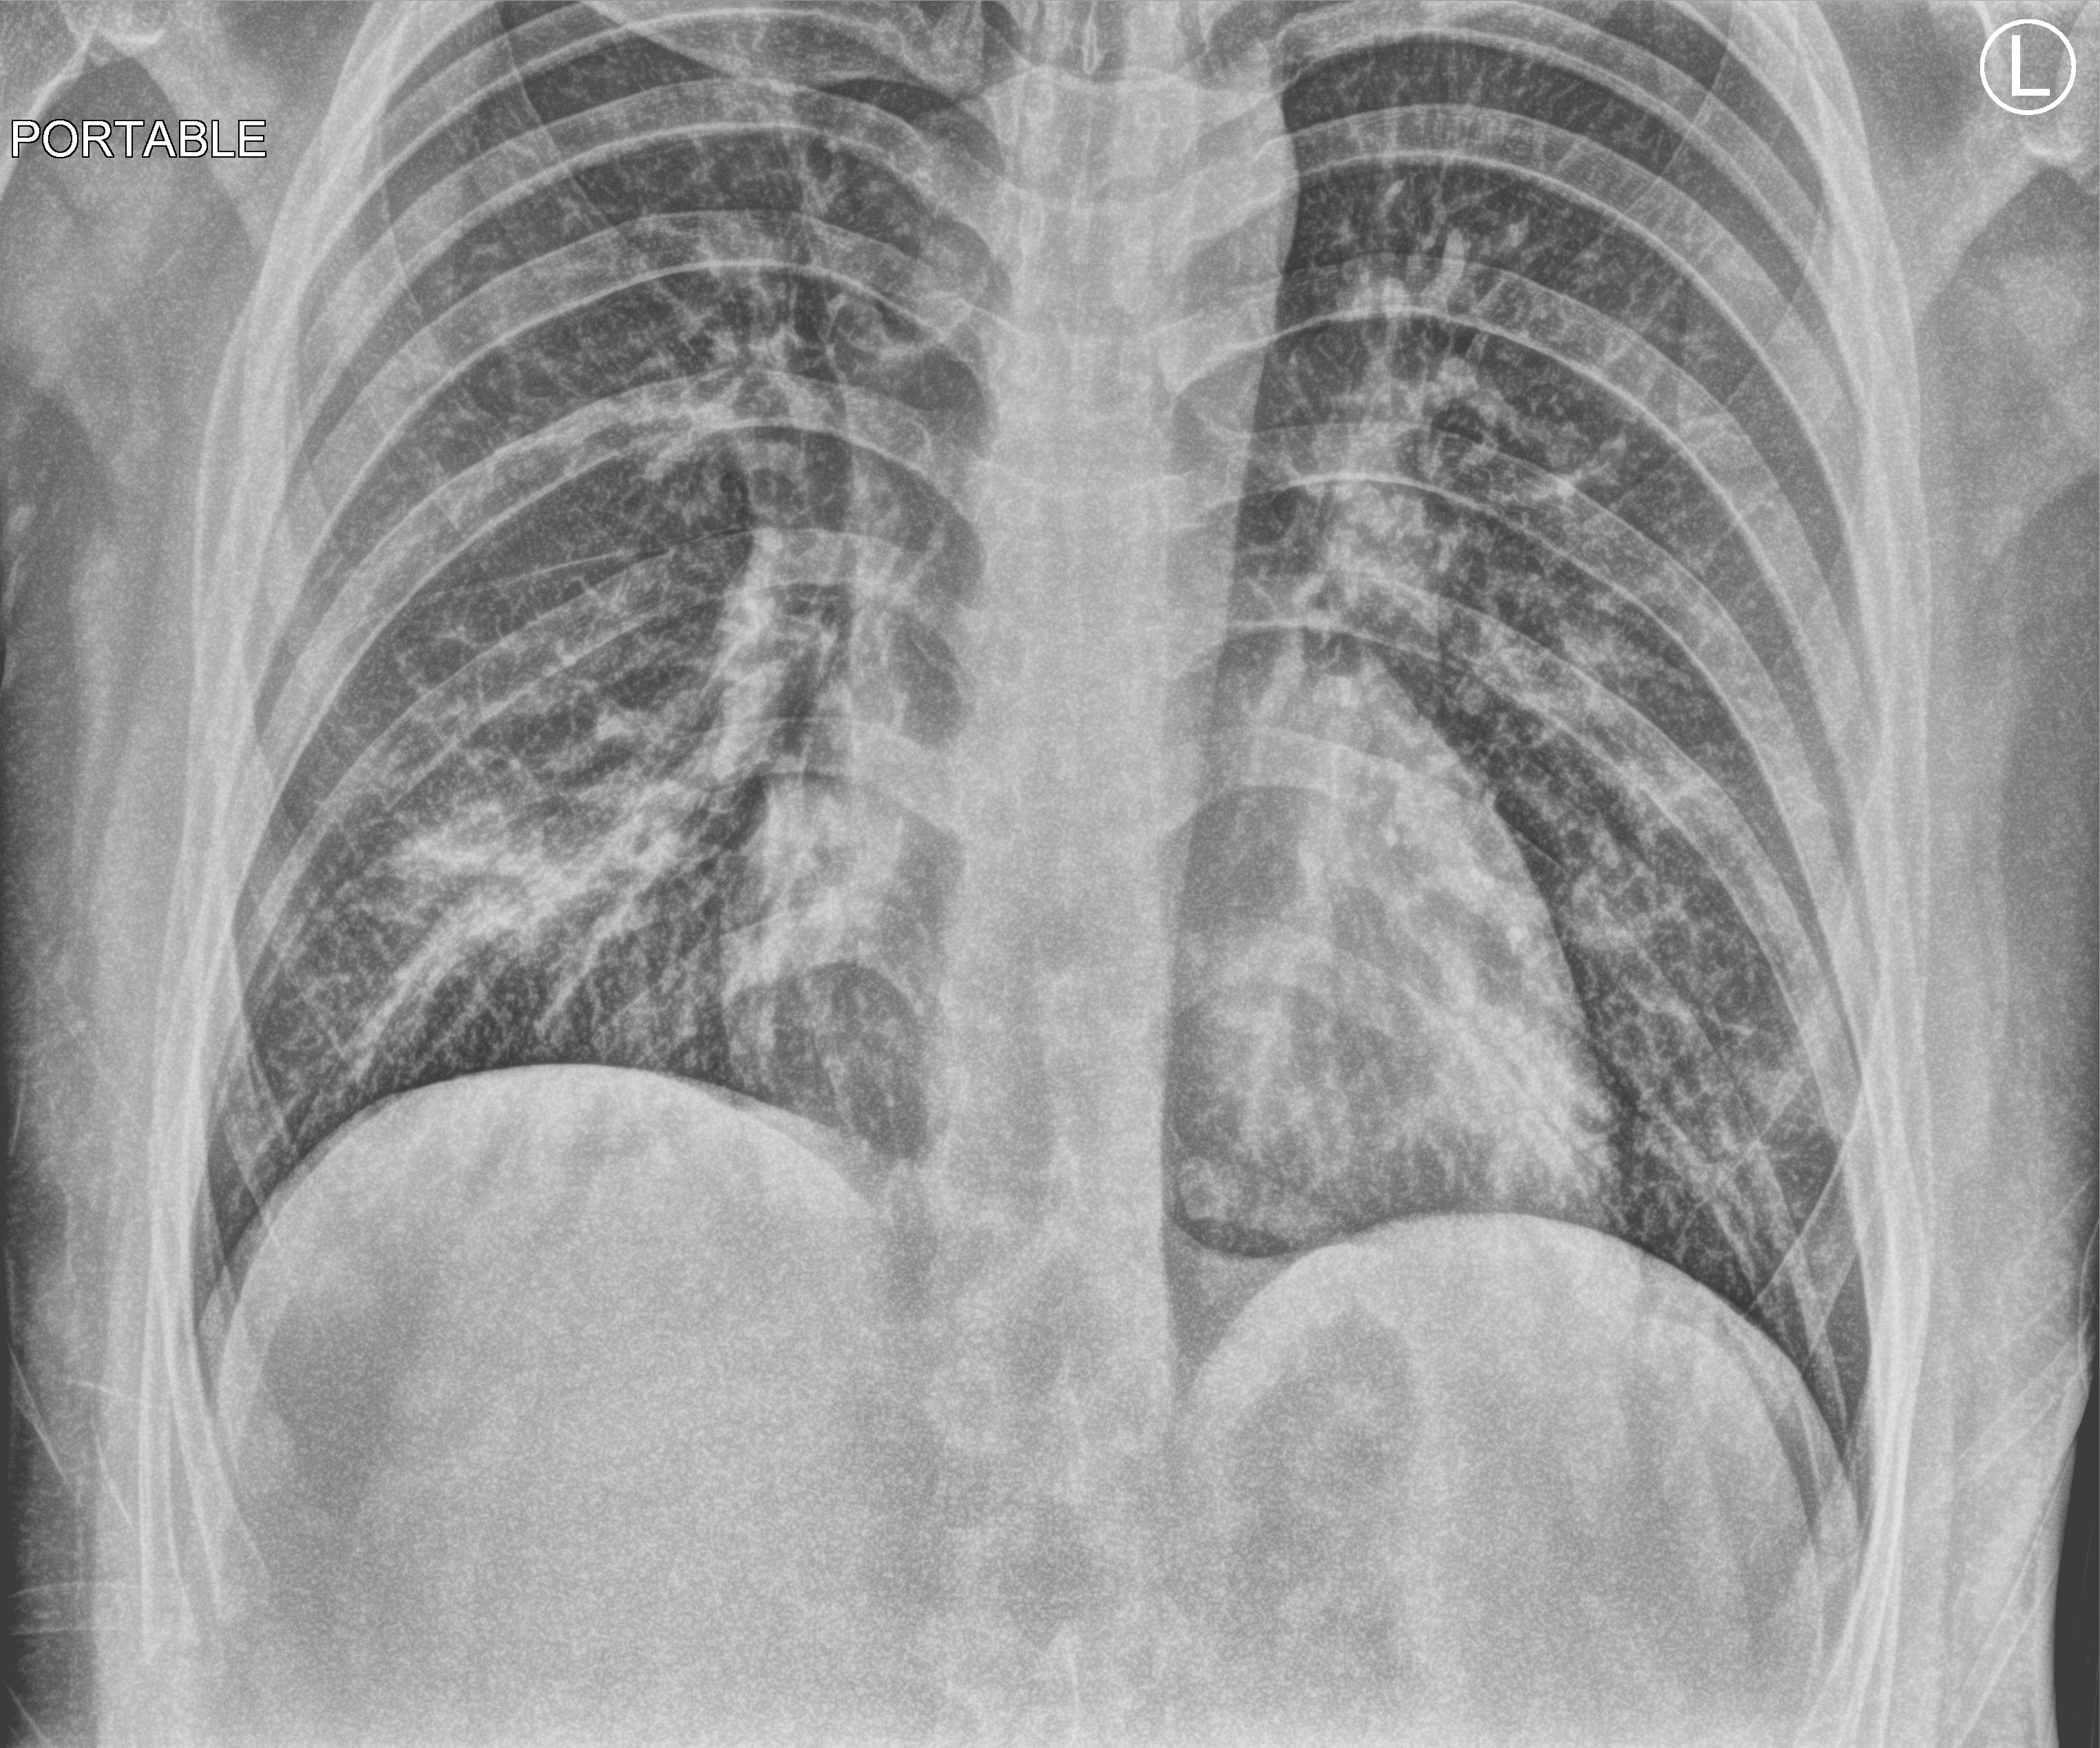
Chest X-ray (portable); anteroposterior (AP) projection. Patient hospitalised with COVID-19; male, aged 18–59 years.
Admission-level facts for this patient (not findings on this image; timing relative to this image not recorded): length of hospital stay: 6 days; diabetes (admission record): no.